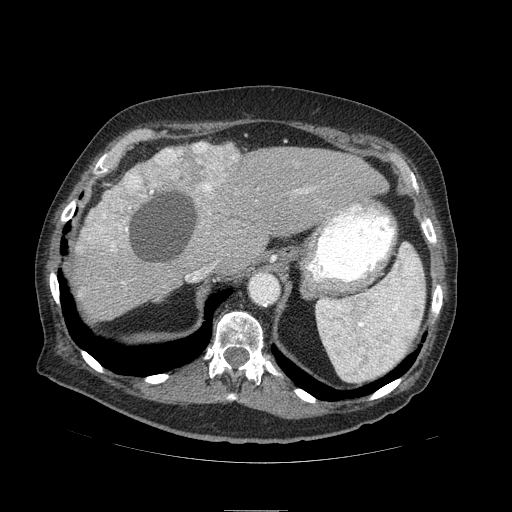
Contrast-enhanced abdominal CT (liver protocol), one axial slice; position 69 of 103 along the scan axis; reconstruction kernel STANDARD; 120 kVp; soft-tissue window (W 400 / L 40 HU); 512 × 512 image matrix, field of view 440 × 440 mm. From the clinical record (not read from this slice): diagnosis: hepatocellular carcinoma (patient treated with transarterial chemoembolisation; whether this scan precedes or follows treatment is not stated here); TNM stage (as recorded): Stage-IIIA; Child-Pugh class: B.
Annotated regions visible in this slice (semi-automatically segmented with operator editing):
- liver parenchyma outside the tumour (the mass and vessels are separate outlines, so this box may not span the whole liver): bounding box <70,142,388,320> (left, top, right, bottom; pixels)
- mass: <81,142,240,257>
- liver vessels: <186,192,301,277>